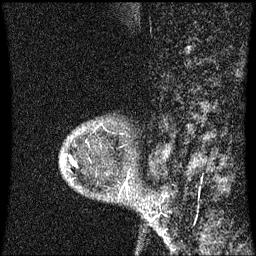
Breast MRI (dynamic contrast-enhanced), one sagittal slice. Dynamic contrast-enhanced series, image 2 of 3 at this slice position (ordered by acquisition). 1.5 T. TE 4.2 ms, TR 8.9 ms. 2 mm slice thickness. 256 × 256 image matrix, field of view 200 × 200 mm. Female patient, age 53 years. Case-level facts recorded for this patient, not image findings: setting: breast cancer imaged before/during neoadjuvant chemotherapy; receptor status: HR-positive, HER2-negative.
Outlined on this slice (semi-automatically segmented with operator editing):
- analysis volume of interest (the breast-tissue region the enhancement analysis was run in; not a lesion): box from (x=64, y=158) to (x=129, y=201) px
- tumour enhancement mask (voxels above the 70 % enhancement threshold inside the analysis volume of interest): (x=74, y=164)–(x=77, y=167)